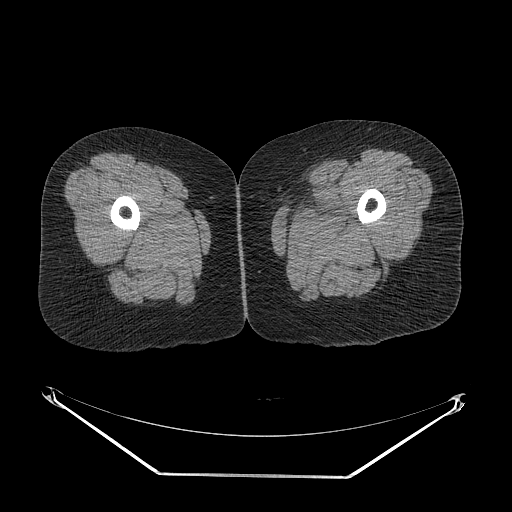
CT of an extremity soft-tissue mass (from a PET/CT study), one axial slice. Reconstruction kernel STANDARD. 140 kVp. Soft-tissue window (W 400 / L 40 HU). 3.75 mm slice thickness. 512 × 512 image matrix. Female patient. Case-level facts recorded for this patient, not image findings: histological type: myxofibrosarcoma; grade: intermediate; site of the primary tumour: left thigh.
Outlined on this slice (expert contour drawn on MRI and transferred to this co-registered scan by the dataset authors):
- gross tumour volume including surrounding oedema: bounding box [x1, y1, x2, y2] px = [283, 196, 348, 236]